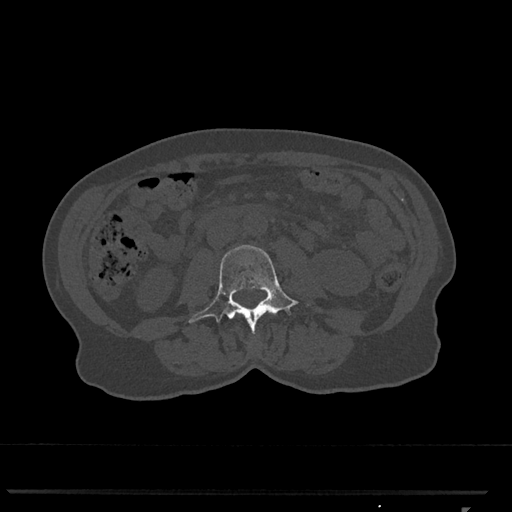
CT including the spine, one axial slice. Position 277 of 793 along the scan axis. 120 kVp. Bone window (W 1800 / L 400 HU). 0.5 mm slice thickness. 512 × 512 image matrix, field of view 380 × 380 mm. Female patient, age 62 years. From the clinical record (not read from this slice): primary cancer: renal.
Structures marked on this image (semi-automatic segmentation, software-assisted and operator-edited):
- L3 vertebra: box from (x=188, y=245) to (x=309, y=333) px